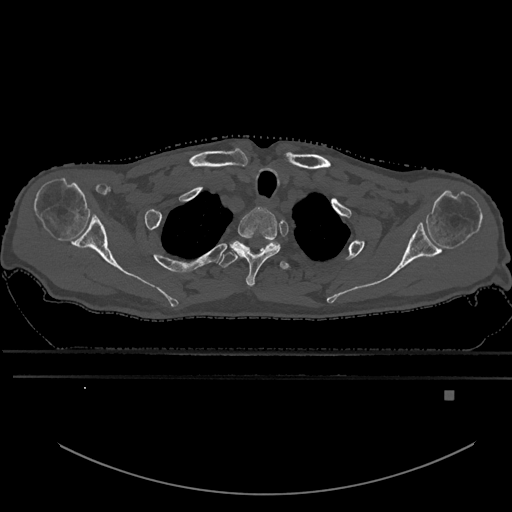
CT including the spine, one axial slice. Slice 523 of 969 in the series (ordered by position). Bone window (W 1800 / L 400 HU). 0.5 mm slice thickness. 512 × 512 image matrix, field of view 456 × 456 mm. Male patient, age 82 years. From the clinical record (not read from this slice): primary cancer: prostate; vertebrae with lytic lesions (as recorded): T11, T9, T8, T2.
Outlined on this slice (semi-automatically segmented with operator editing):
- T1 vertebra: box from (x=231, y=207) to (x=281, y=287) px
- T2 vertebra: (x=219, y=238)–(x=280, y=267)